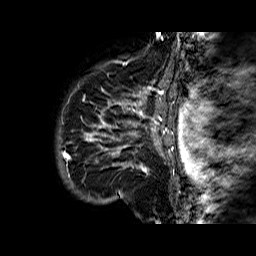
Breast MRI (dynamic contrast-enhanced), one sagittal slice. Slice 55 of 60 in the series (ordered by position). Dynamic contrast-enhanced series, time point 2 of 6 at this slice position (early post-contrast). 1.5 T. TE 6.3 ms, TR 32.4 ms. 4 mm slice thickness. 256 × 256 image matrix. Female patient. From the clinical record (not read from this slice): setting: breast cancer imaged before/during neoadjuvant chemotherapy; receptor status: HR-positive, HER2-negative.
Annotated regions visible in this slice (semi-automatically segmented with operator editing):
- analysis volume of interest (the breast-tissue region the enhancement analysis was run in; not a lesion): bounding box (x1, y1, x2, y2) in pixels: (68, 72, 177, 183)
- tumour enhancement mask (voxels above the 100 % enhancement threshold inside the analysis volume of interest): (83, 87, 174, 172)